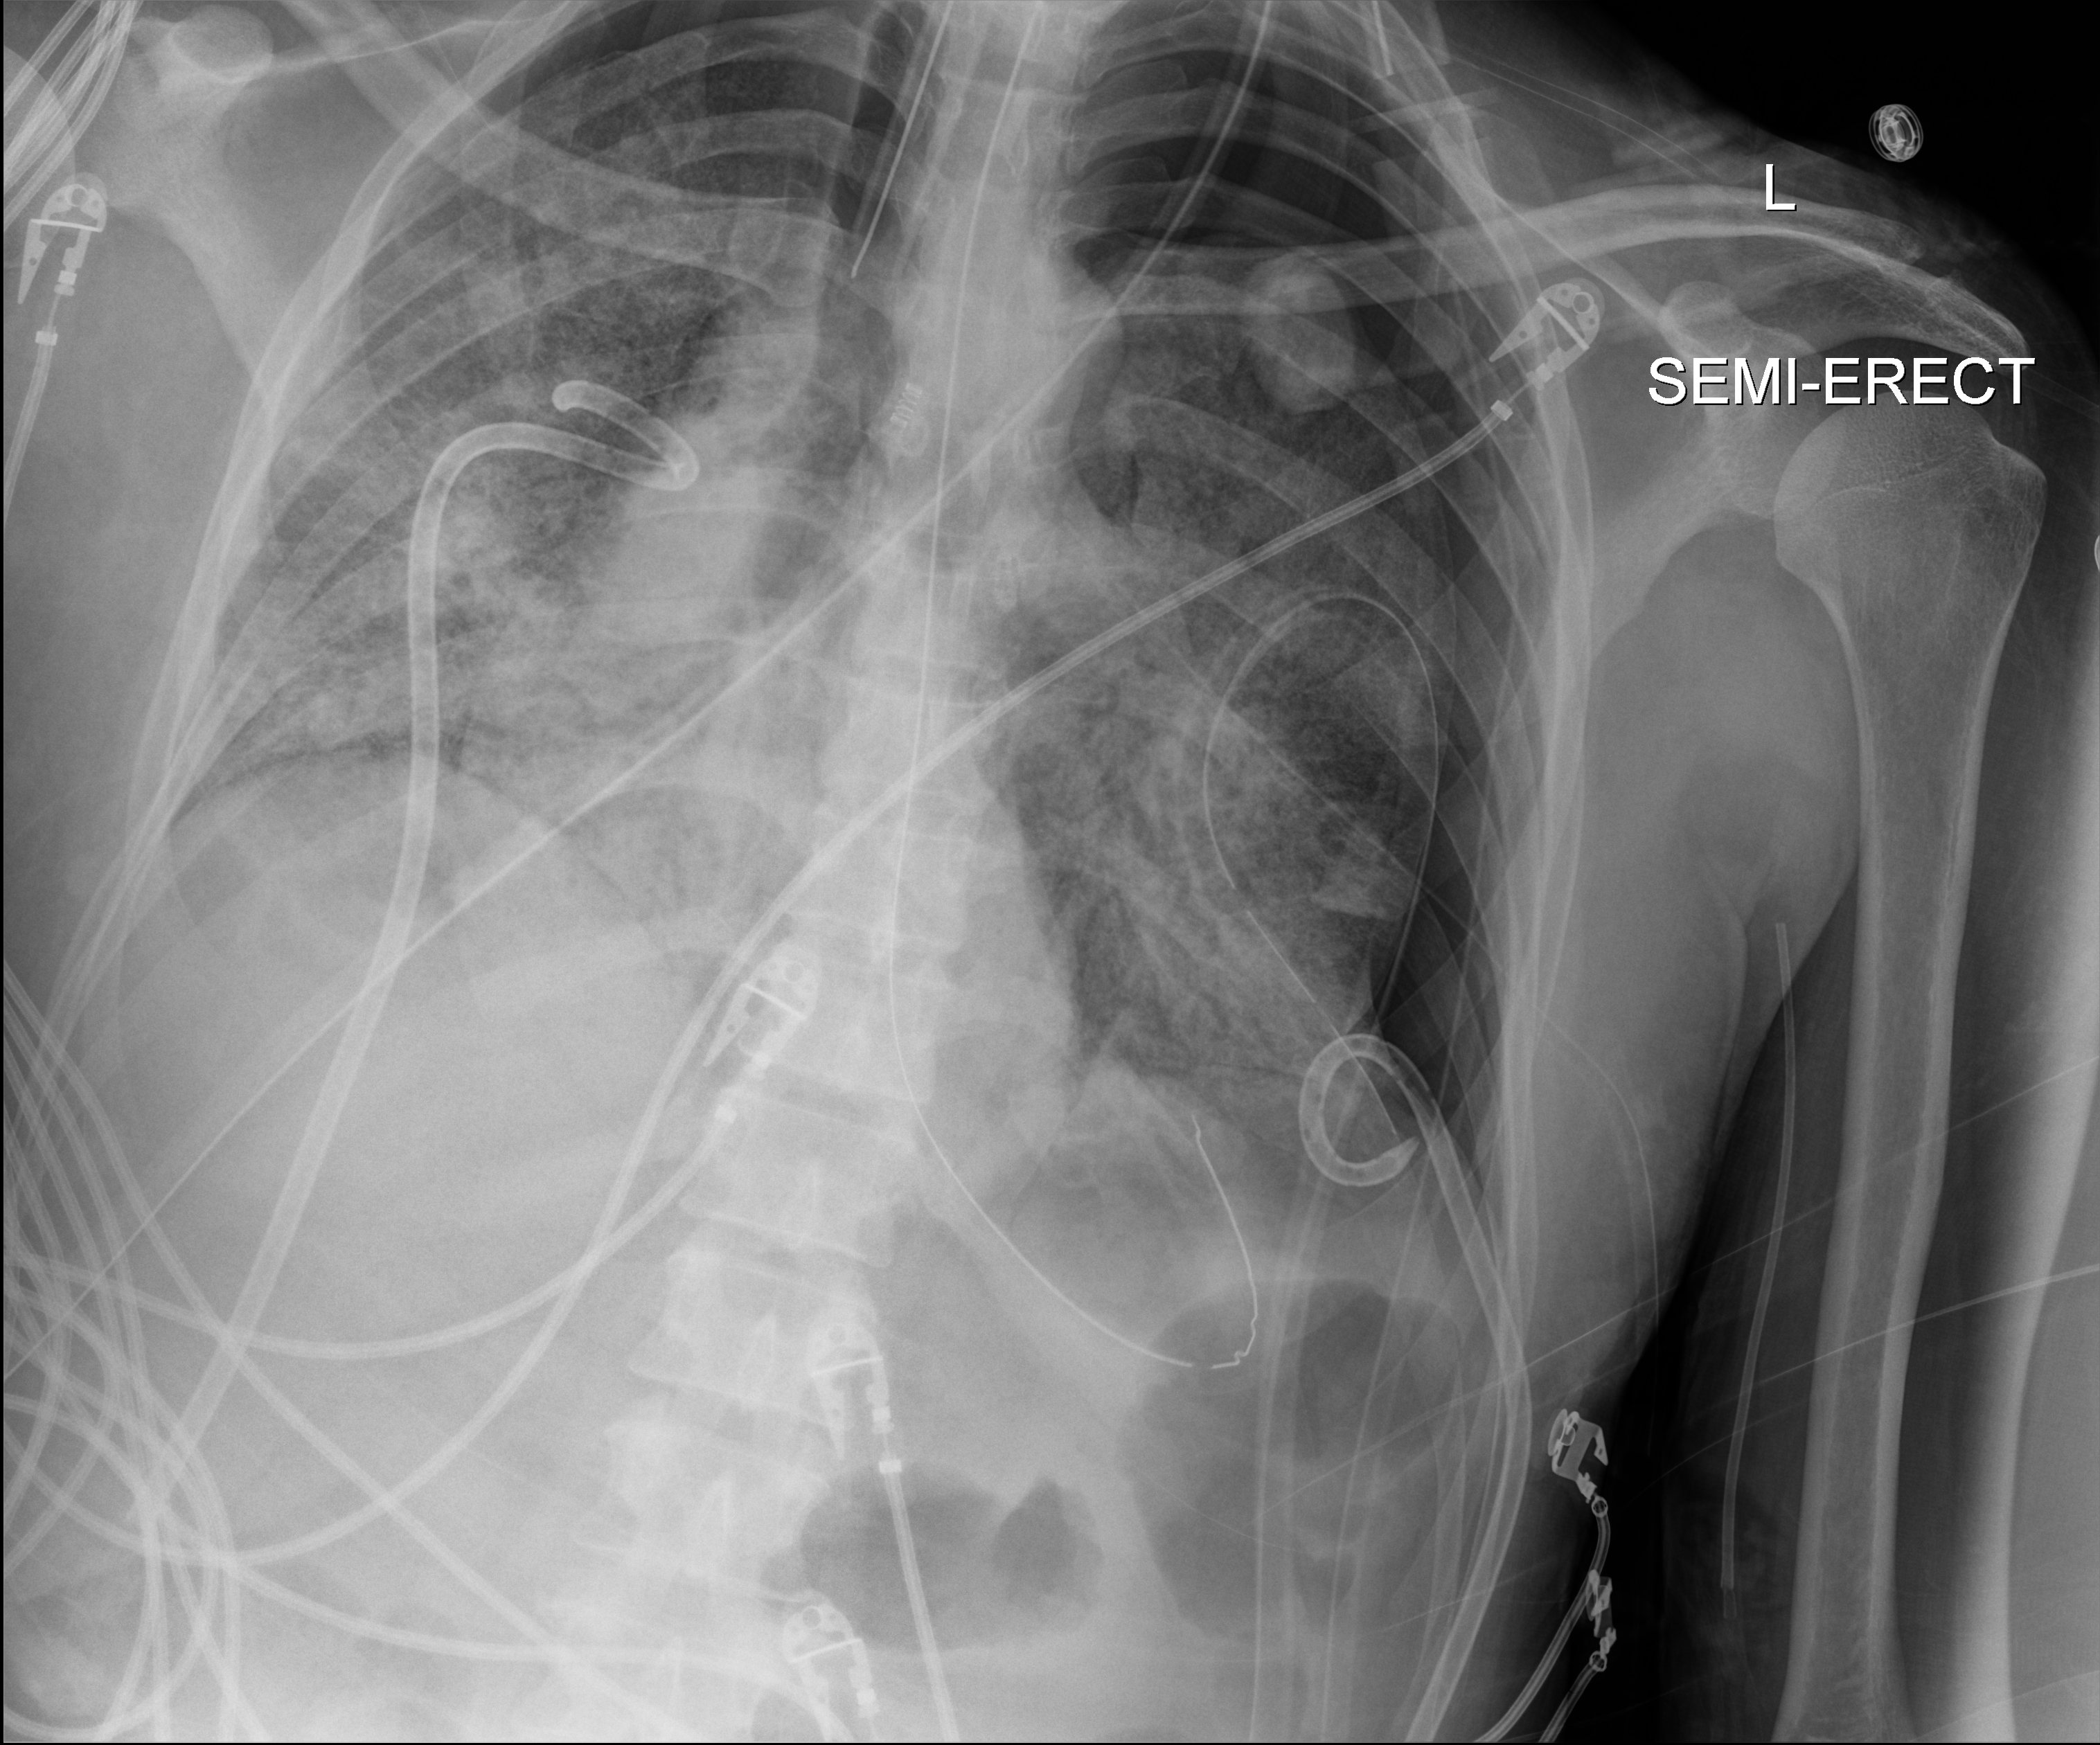
Portable chest radiograph; anteroposterior (AP) projection. Patient hospitalised with COVID-19, aged 18–59 years.
Hospital-stay facts (about this admission, not read from this image; timing relative to this image not recorded):
- admitted to intensive care during this hospital stay: yes